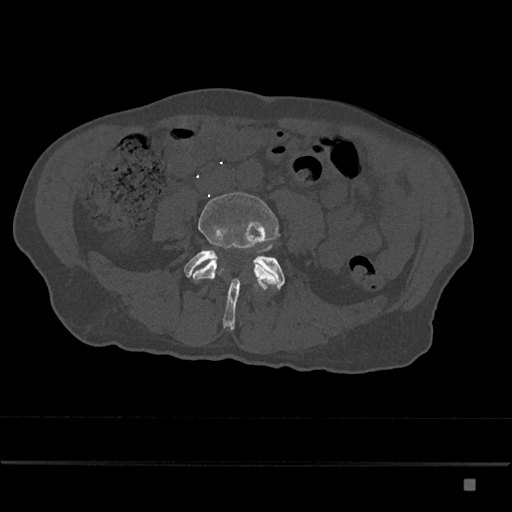
CT including the spine, one axial slice; slice 312 of 797 in the series (ordered by position); 120 kVp; bone window (W 1800 / L 400 HU); 0.5 mm slice thickness; 512 × 512 image matrix. Male patient, age 72 years. Case-level facts recorded for this patient, not image findings: primary cancer: prostate.
Annotated regions visible in this slice (semi-automatic segmentation, software-assisted and operator-edited):
- L4 vertebra: box from (x=190, y=192) to (x=279, y=287) px
- L5 vertebra: (x=184, y=250)–(x=285, y=330)